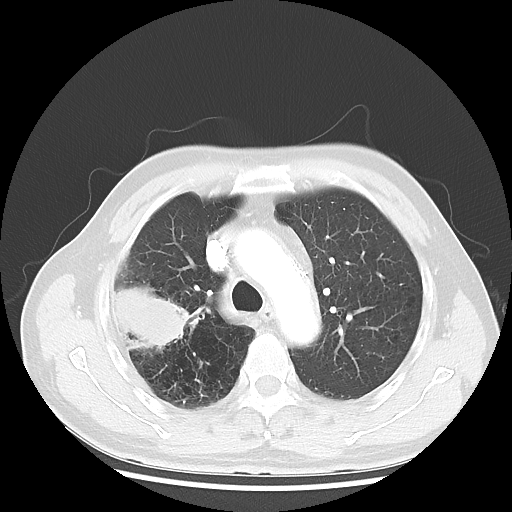
Chest CT, one axial slice; position 36 of 50 along the scan axis; reconstruction kernel LUNG; 120 kVp; lung window (W 1500 / L -600 HU); 5 mm slice thickness; 512 × 512 image matrix, field of view 360 × 360 mm. Male patient, age 69 years. Case-level facts recorded for this patient, not image findings: clinical TNM (as recorded): T3 N0 M0; histopathological grade: G3.
Outlined on this slice (bounding box drawn by a radiologist):
- lung tumour (recorded histology: adenocarcinoma): bounding box <114,281,195,354> (left, top, right, bottom; pixels)